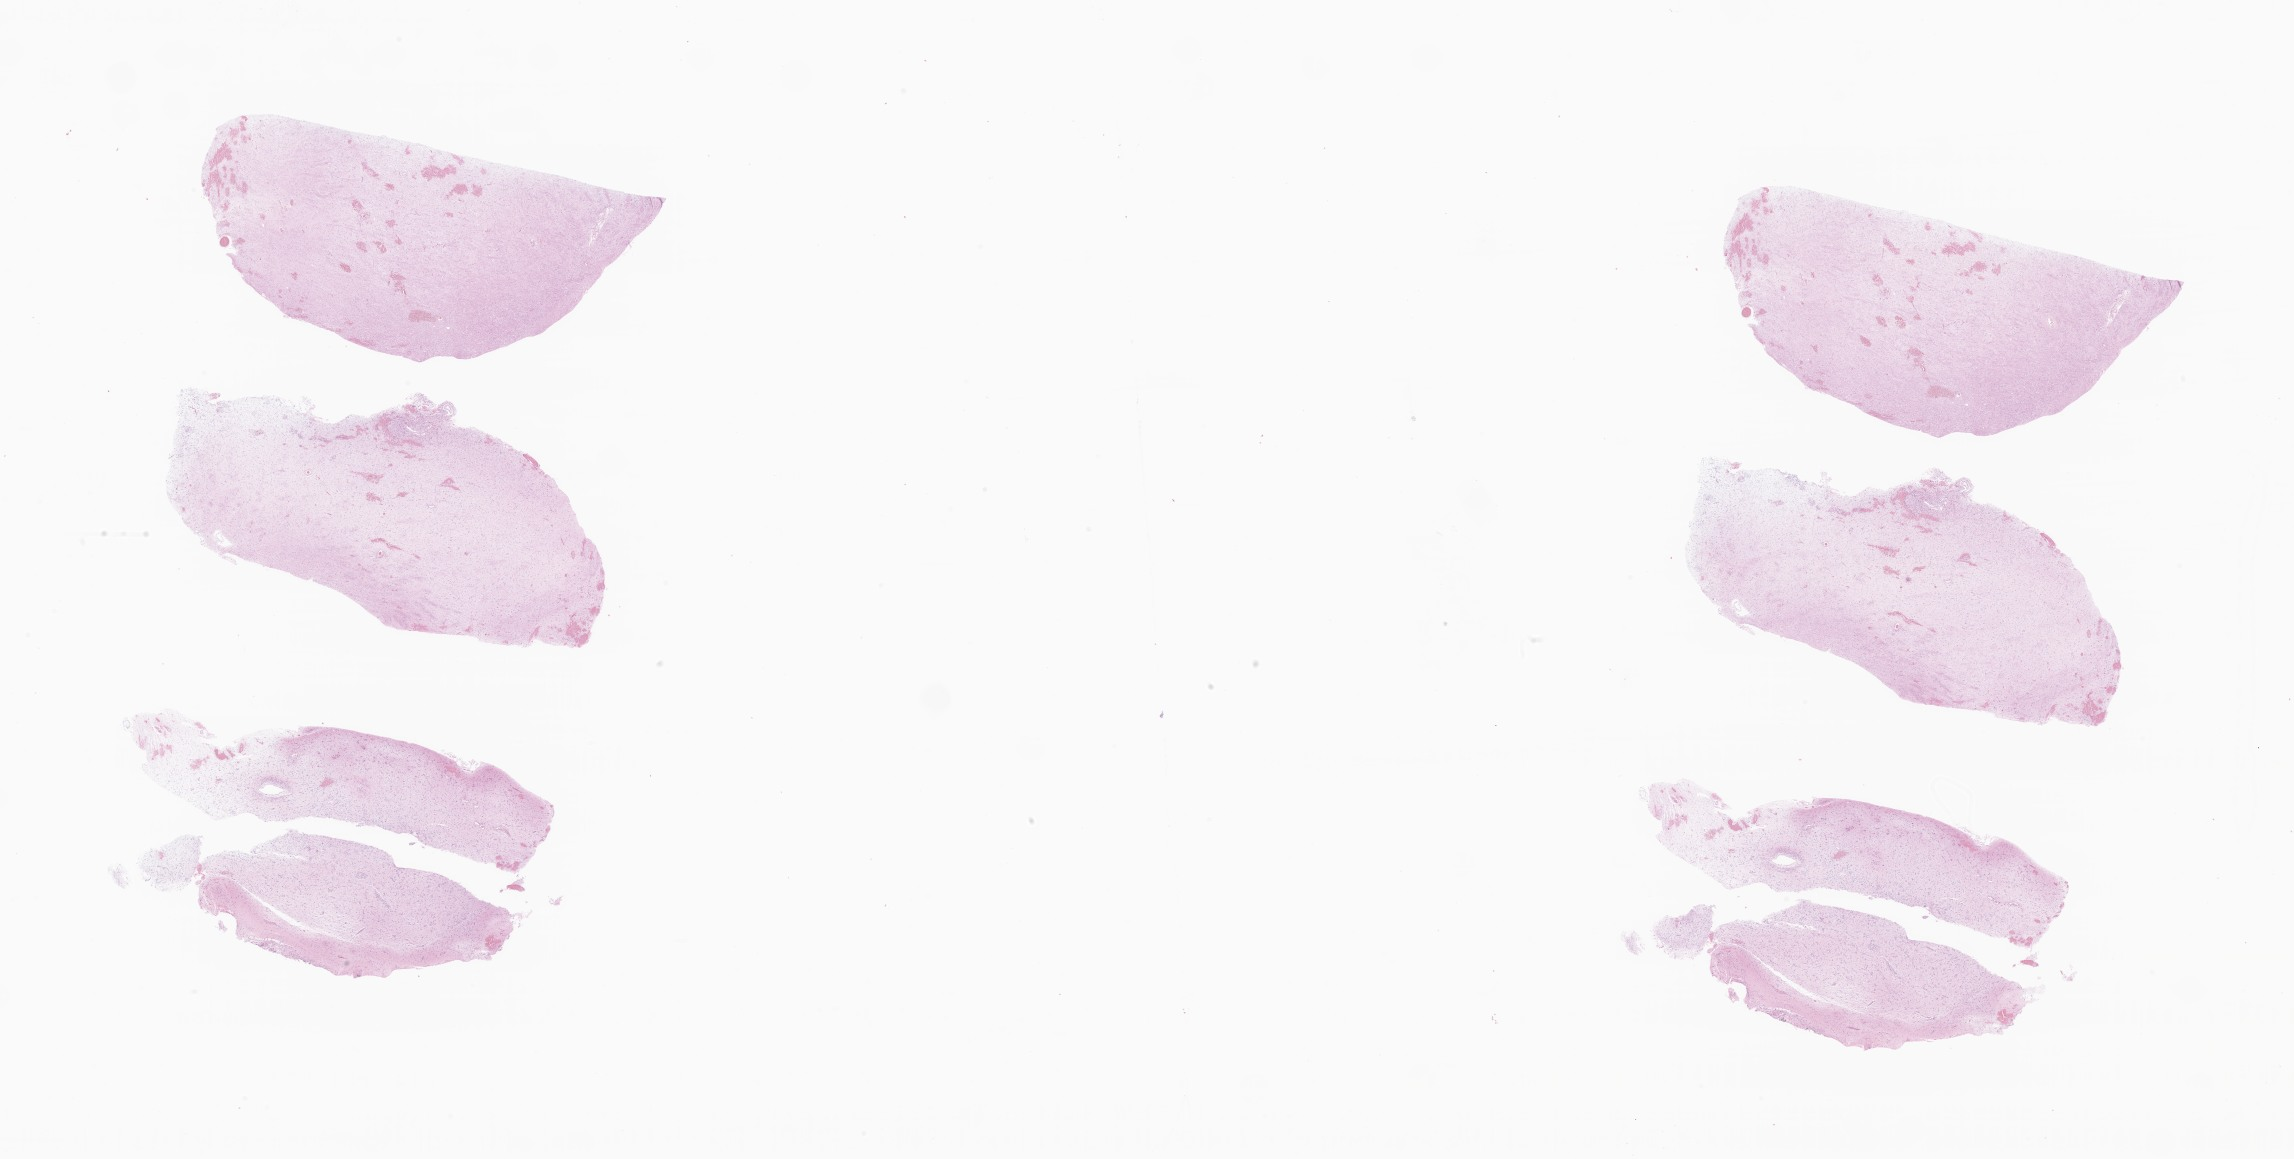
Whole-slide image, haematoxylin and eosin stain of tumor tissue from the temporal lobe, a low-resolution overview of the entire scanned area, about 38.7 x 19.5 mm. Formalin-fixed paraffin-embedded section. Patient: female, age 239 months (19 years 11 months).
Diagnosis (ICD-O-3 morphology term): Astrocytoma, NOS.